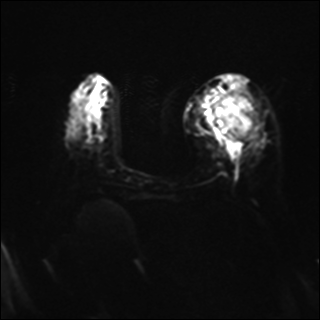
Breast MRI, one axial slice. Diffusion-weighted series; image 2 of 4 stored at this slice position (different b-values; order by instance number). 1.5 T. 320 × 320 image matrix, field of view 320 × 320 mm. Female patient.
Structures marked on this image (manually delineated by an expert):
- tumour on diffusion-weighted imaging: bounding box [x1, y1, x2, y2] px = [214, 93, 258, 139]